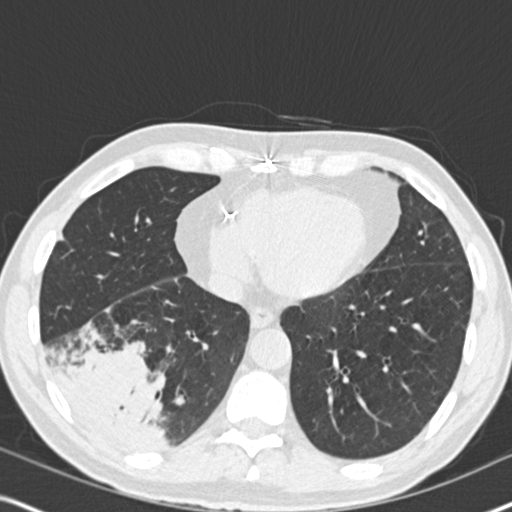
Low-dose screening chest CT, one axial slice; slice 68 of 182 in the series (ordered by position); reconstruction kernel B30f; 120 kVp; lung window (W 1500 / L -600 HU); 2 mm slice thickness; 512 × 512 image matrix, field of view 330 × 330 mm.
Annotated regions visible in this slice (manually delineated by an expert):
- lesion 1 (tumor, lower lobe of right lung): bounding box [x1, y1, x2, y2] px = [60, 352, 167, 448]